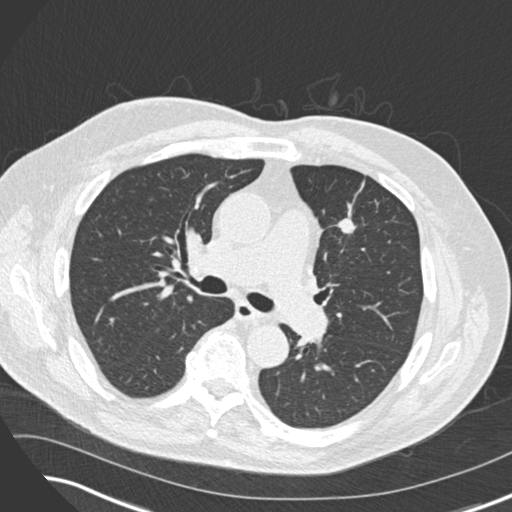
Low-dose screening chest CT, one axial slice; position 100 of 169 along the scan axis; lung window (W 1500 / L -600 HU); 2 mm slice thickness; 512 × 512 image matrix, field of view 360 × 360 mm.
Outlined on this slice (expert manual segmentation):
- lesion 1 (tumor, upper lobe of left lung): bounding box <337,209,356,233> (left, top, right, bottom; pixels)